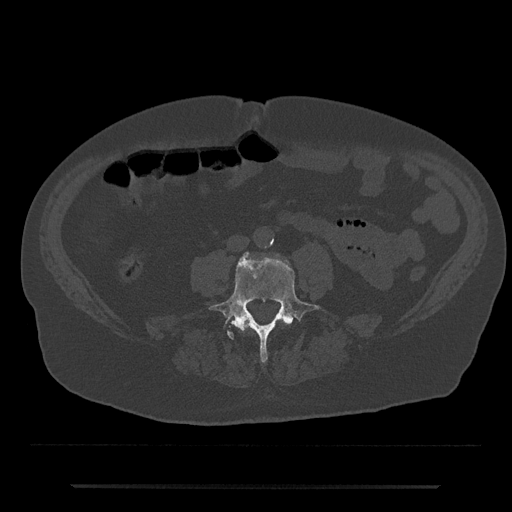
CT including the spine, one axial slice; slice 356 of 797 in the series (ordered by position); reconstruction kernel Br40s/3; 120 kVp; bone window (W 1800 / L 400 HU); 512 × 512 image matrix, field of view 434 × 434 mm. Patient: male, 80 years. Case-level facts recorded for this patient, not image findings: primary cancer: prostate; vertebrae with lytic lesions (as recorded): L1, T11.
Annotated regions visible in this slice (semi-automatically segmented with operator editing):
- L3 vertebra: box from (x=243, y=319) to (x=288, y=329) px
- L4 vertebra: (x=208, y=252)–(x=320, y=362)